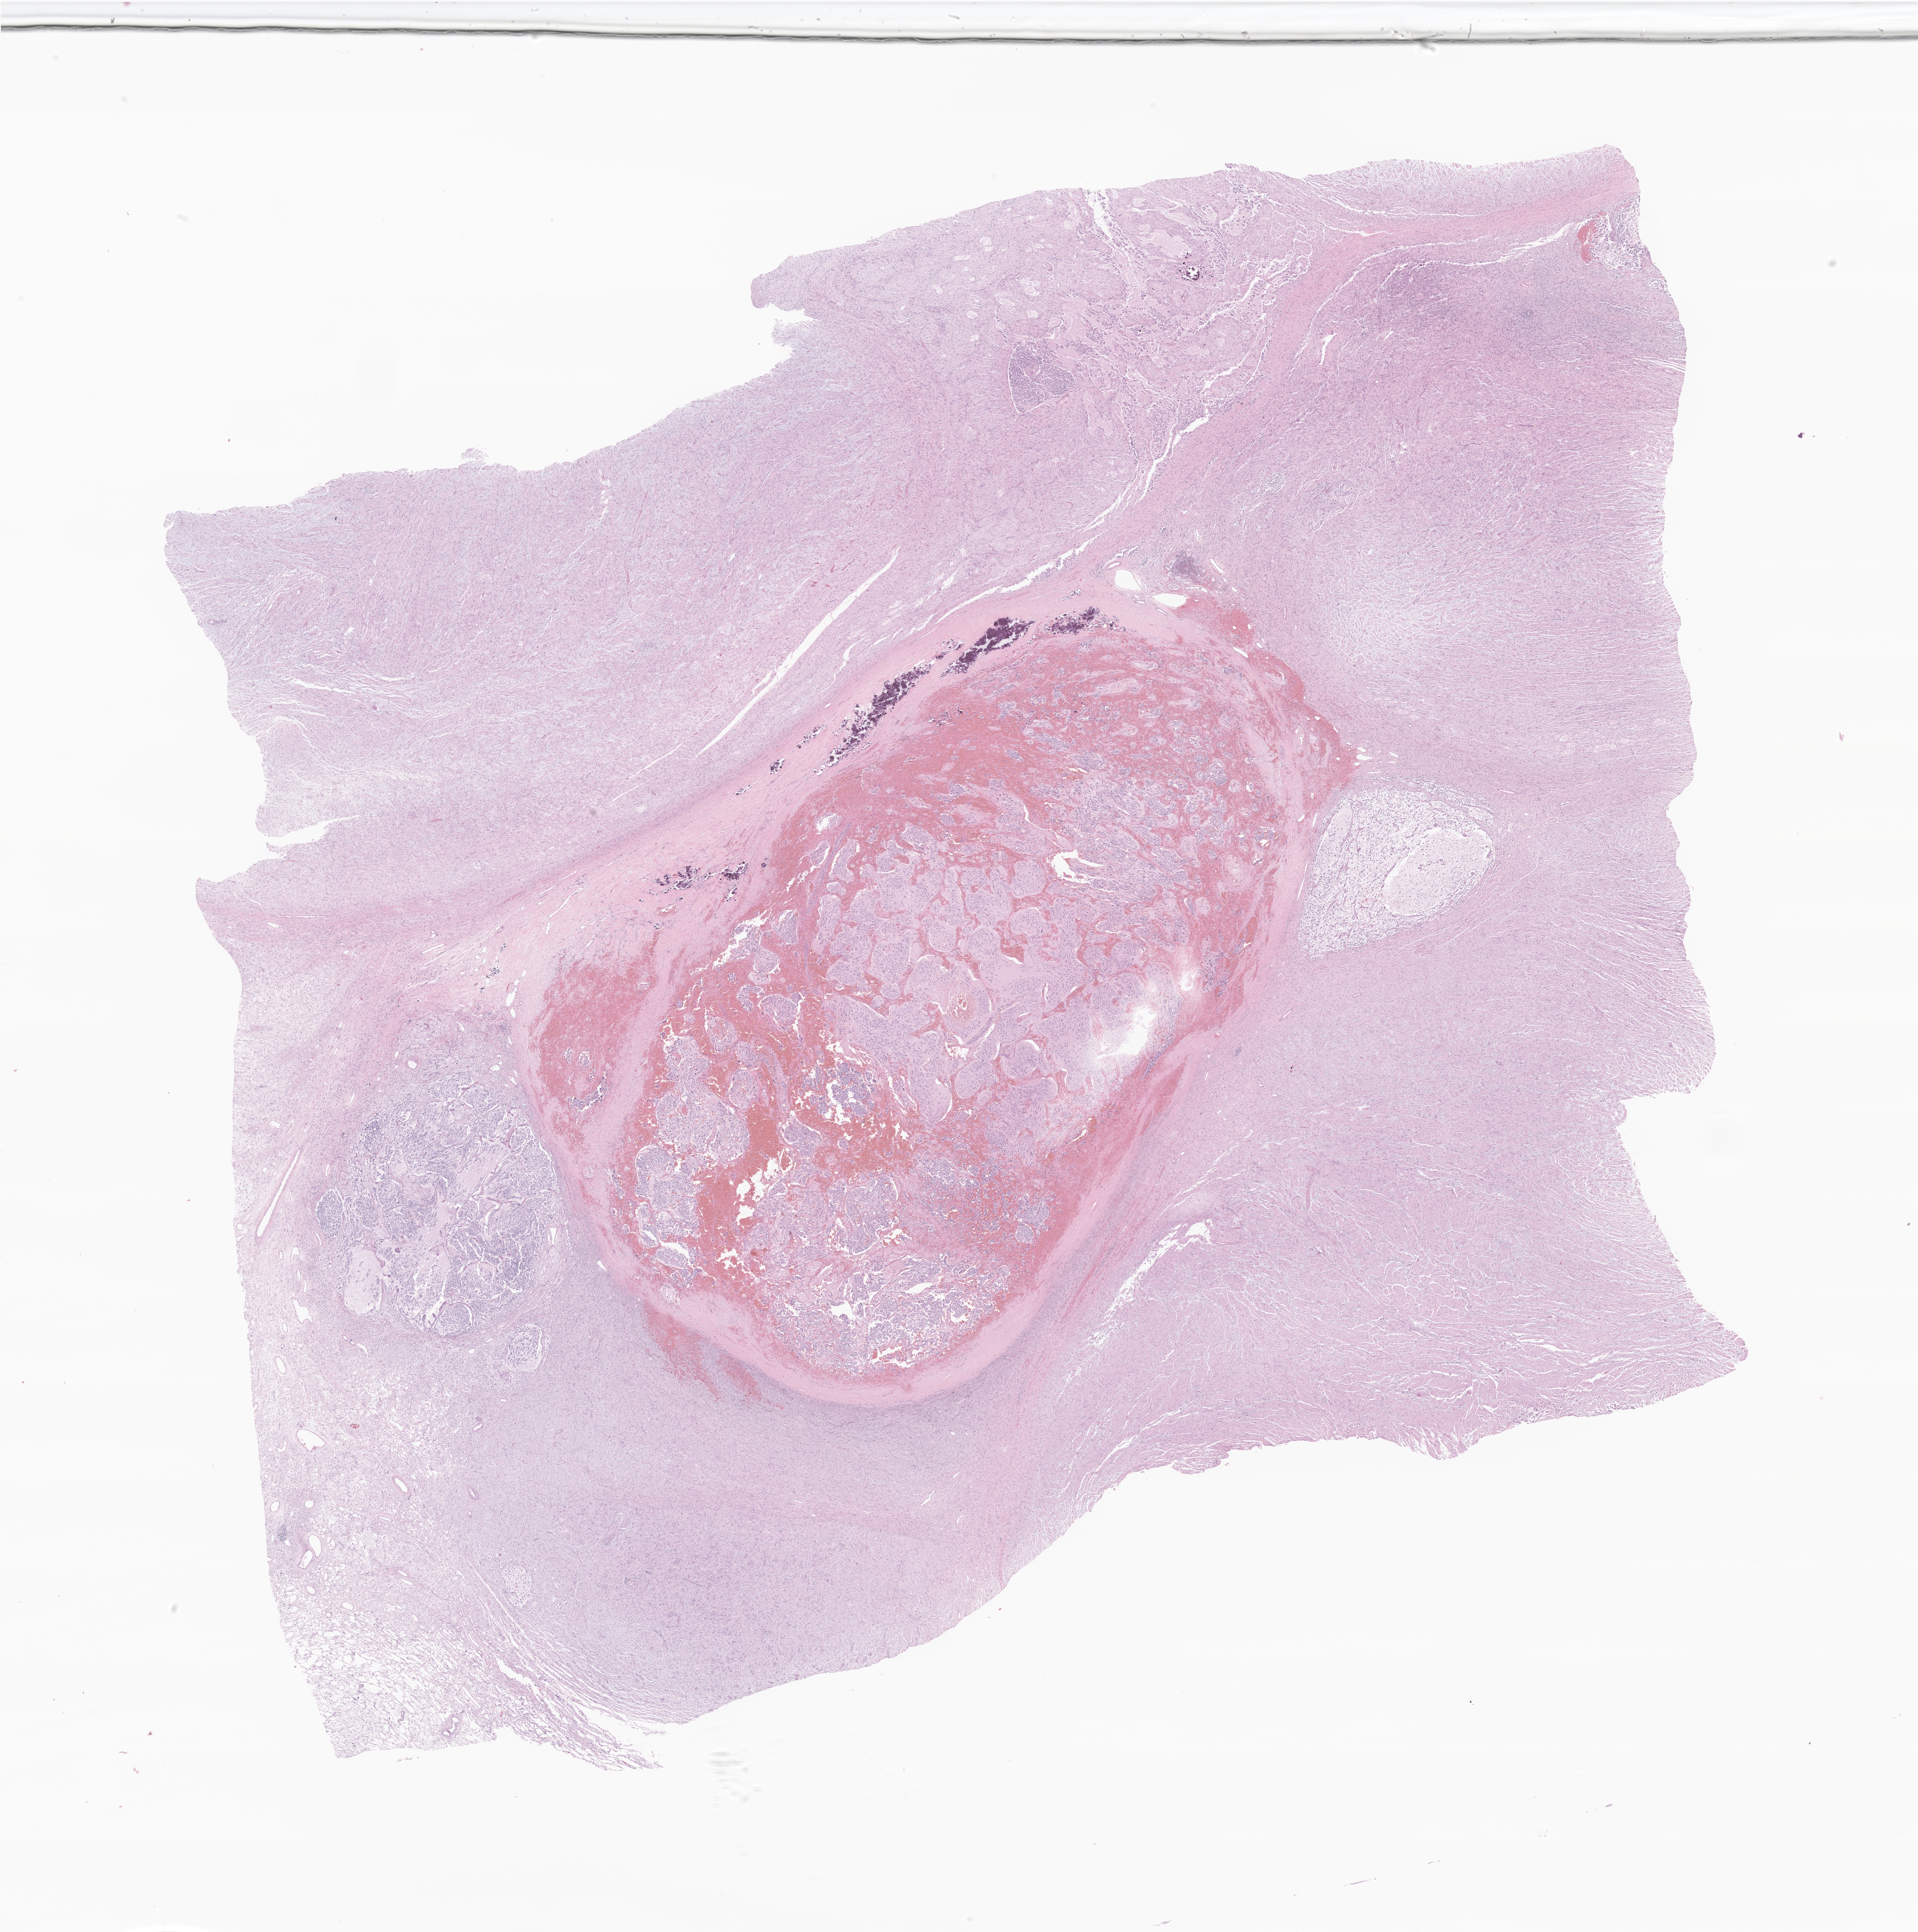
Digitized haematoxylin and eosin-stained section of tumor tissue from the pelvis — a low-resolution overview of the entire scanned area, about 22.5 x 22.6 mm. Formalin-fixed paraffin-embedded section. Patient: female, age 45 months (3 years 9 months).
Diagnosis (ICD-O-3 morphology term): Neuroblastoma, NOS.